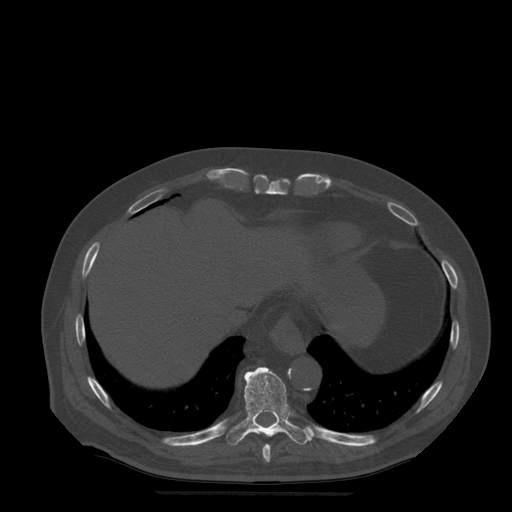
CT including the spine, one axial slice; position 272 of 522 along the scan axis; bone window (W 1800 / L 400 HU); 1.25 mm slice thickness; 512 × 512 image matrix. Patient age 72 years. From the clinical record (not read from this slice): primary cancer: prostate.
Structures marked on this image (semi-automatically segmented with operator editing):
- T10 vertebra: box from (x=227, y=367) to (x=317, y=446) px
- T9 vertebra: (x=263, y=444)–(x=271, y=463)